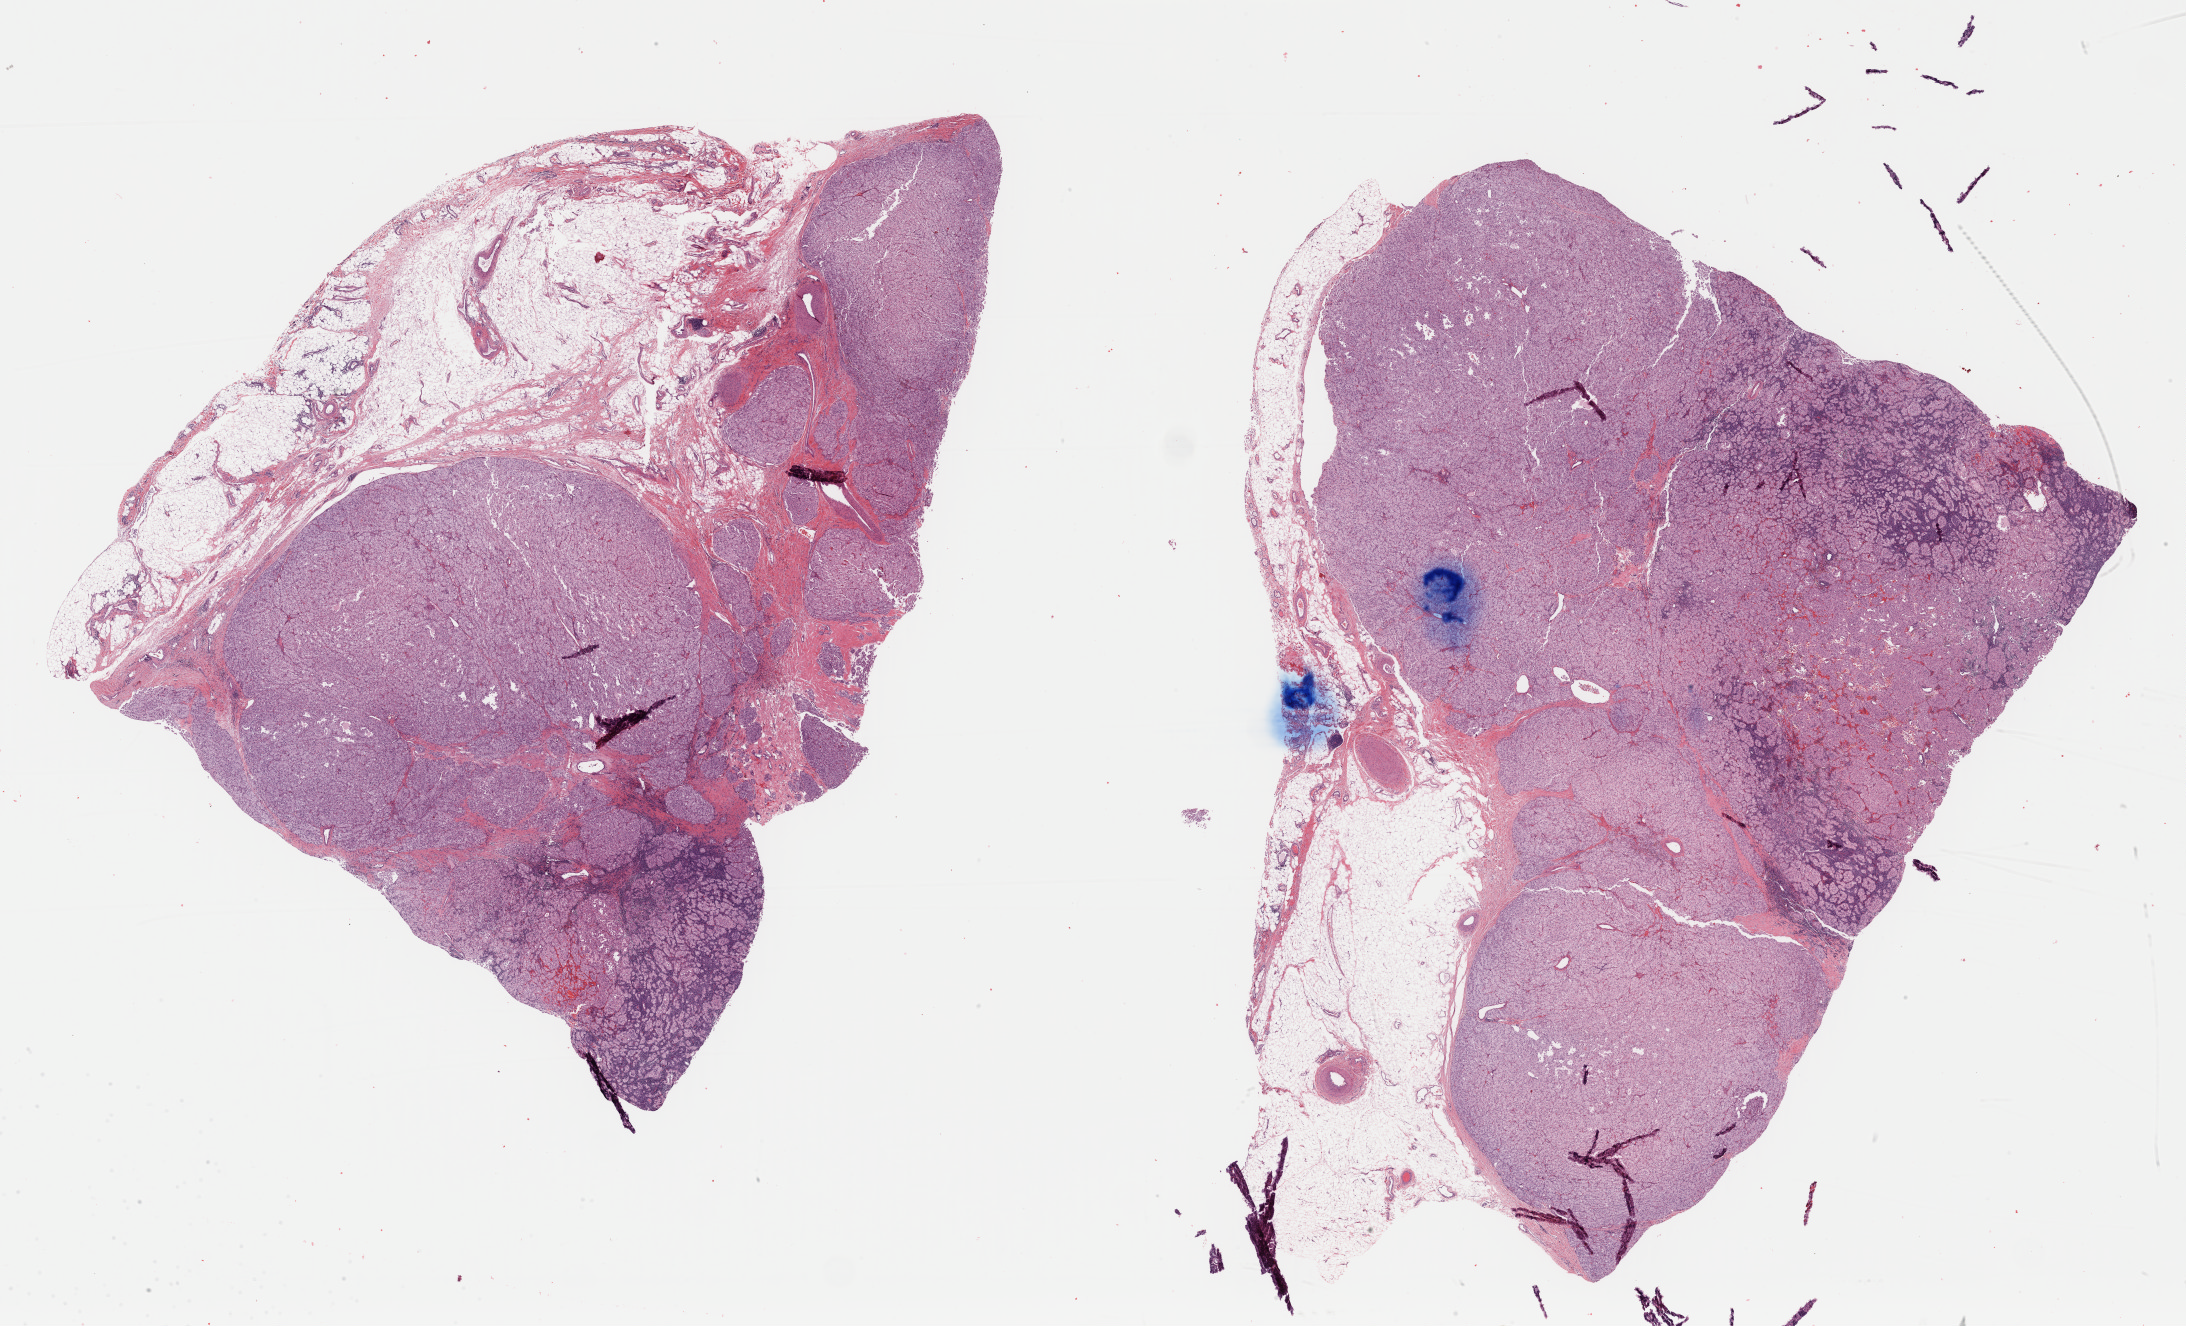
H&E-stained whole-slide image, a low-resolution overview of the entire scanned area, about 34.5 x 20.9 mm, formalin-fixed paraffin-embedded (FFPE) diagnostic section, sample: primary tumour, kidney. Male patient; age at initial diagnosis 29 years.
Laterality: left. AJCC pathologic stage: III (7th edition). Lymph nodes positive (case pathology): 0 of 7 examined. Pathologic diagnosis: Renal cell carcinoma, chromophobe type.